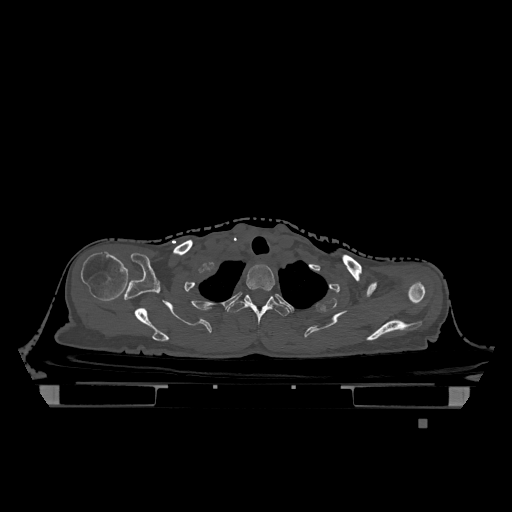
CT including the spine, one axial slice. Position 978 of 1317 along the scan axis. Bone window (W 1800 / L 400 HU). 512 × 512 image matrix, field of view 500 × 500 mm. Patient: female, 74 years. From the clinical record (not read from this slice): primary cancer: lung; vertebrae with lytic lesions (as recorded): T1, T4, T5, T6, L4, L5.
Structures marked on this image (semi-automatically segmented with operator editing):
- T1 vertebra: bounding box [x1, y1, x2, y2] px = [246, 264, 275, 291]
- T2 vertebra: [227, 295, 290, 325]